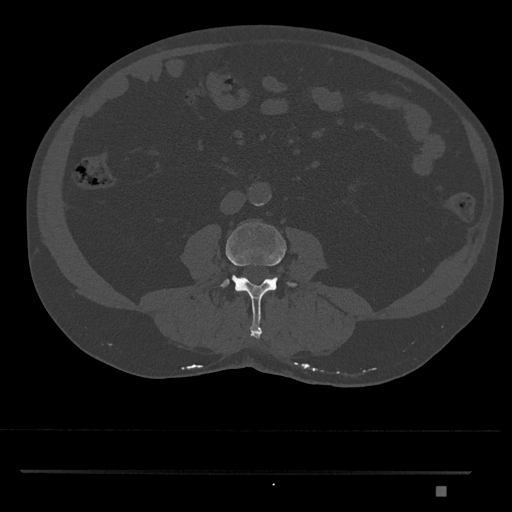
CT including the spine, one axial slice; position 674 of 1134 along the scan axis; bone window (W 1800 / L 400 HU); 512 × 512 image matrix, field of view 429 × 429 mm. Male patient, age 65 years. Case-level facts recorded for this patient, not image findings: primary cancer: prostate.
Structures marked on this image (semi-automatically segmented with operator editing):
- L3 vertebra: bounding box <219,222,298,339> (left, top, right, bottom; pixels)